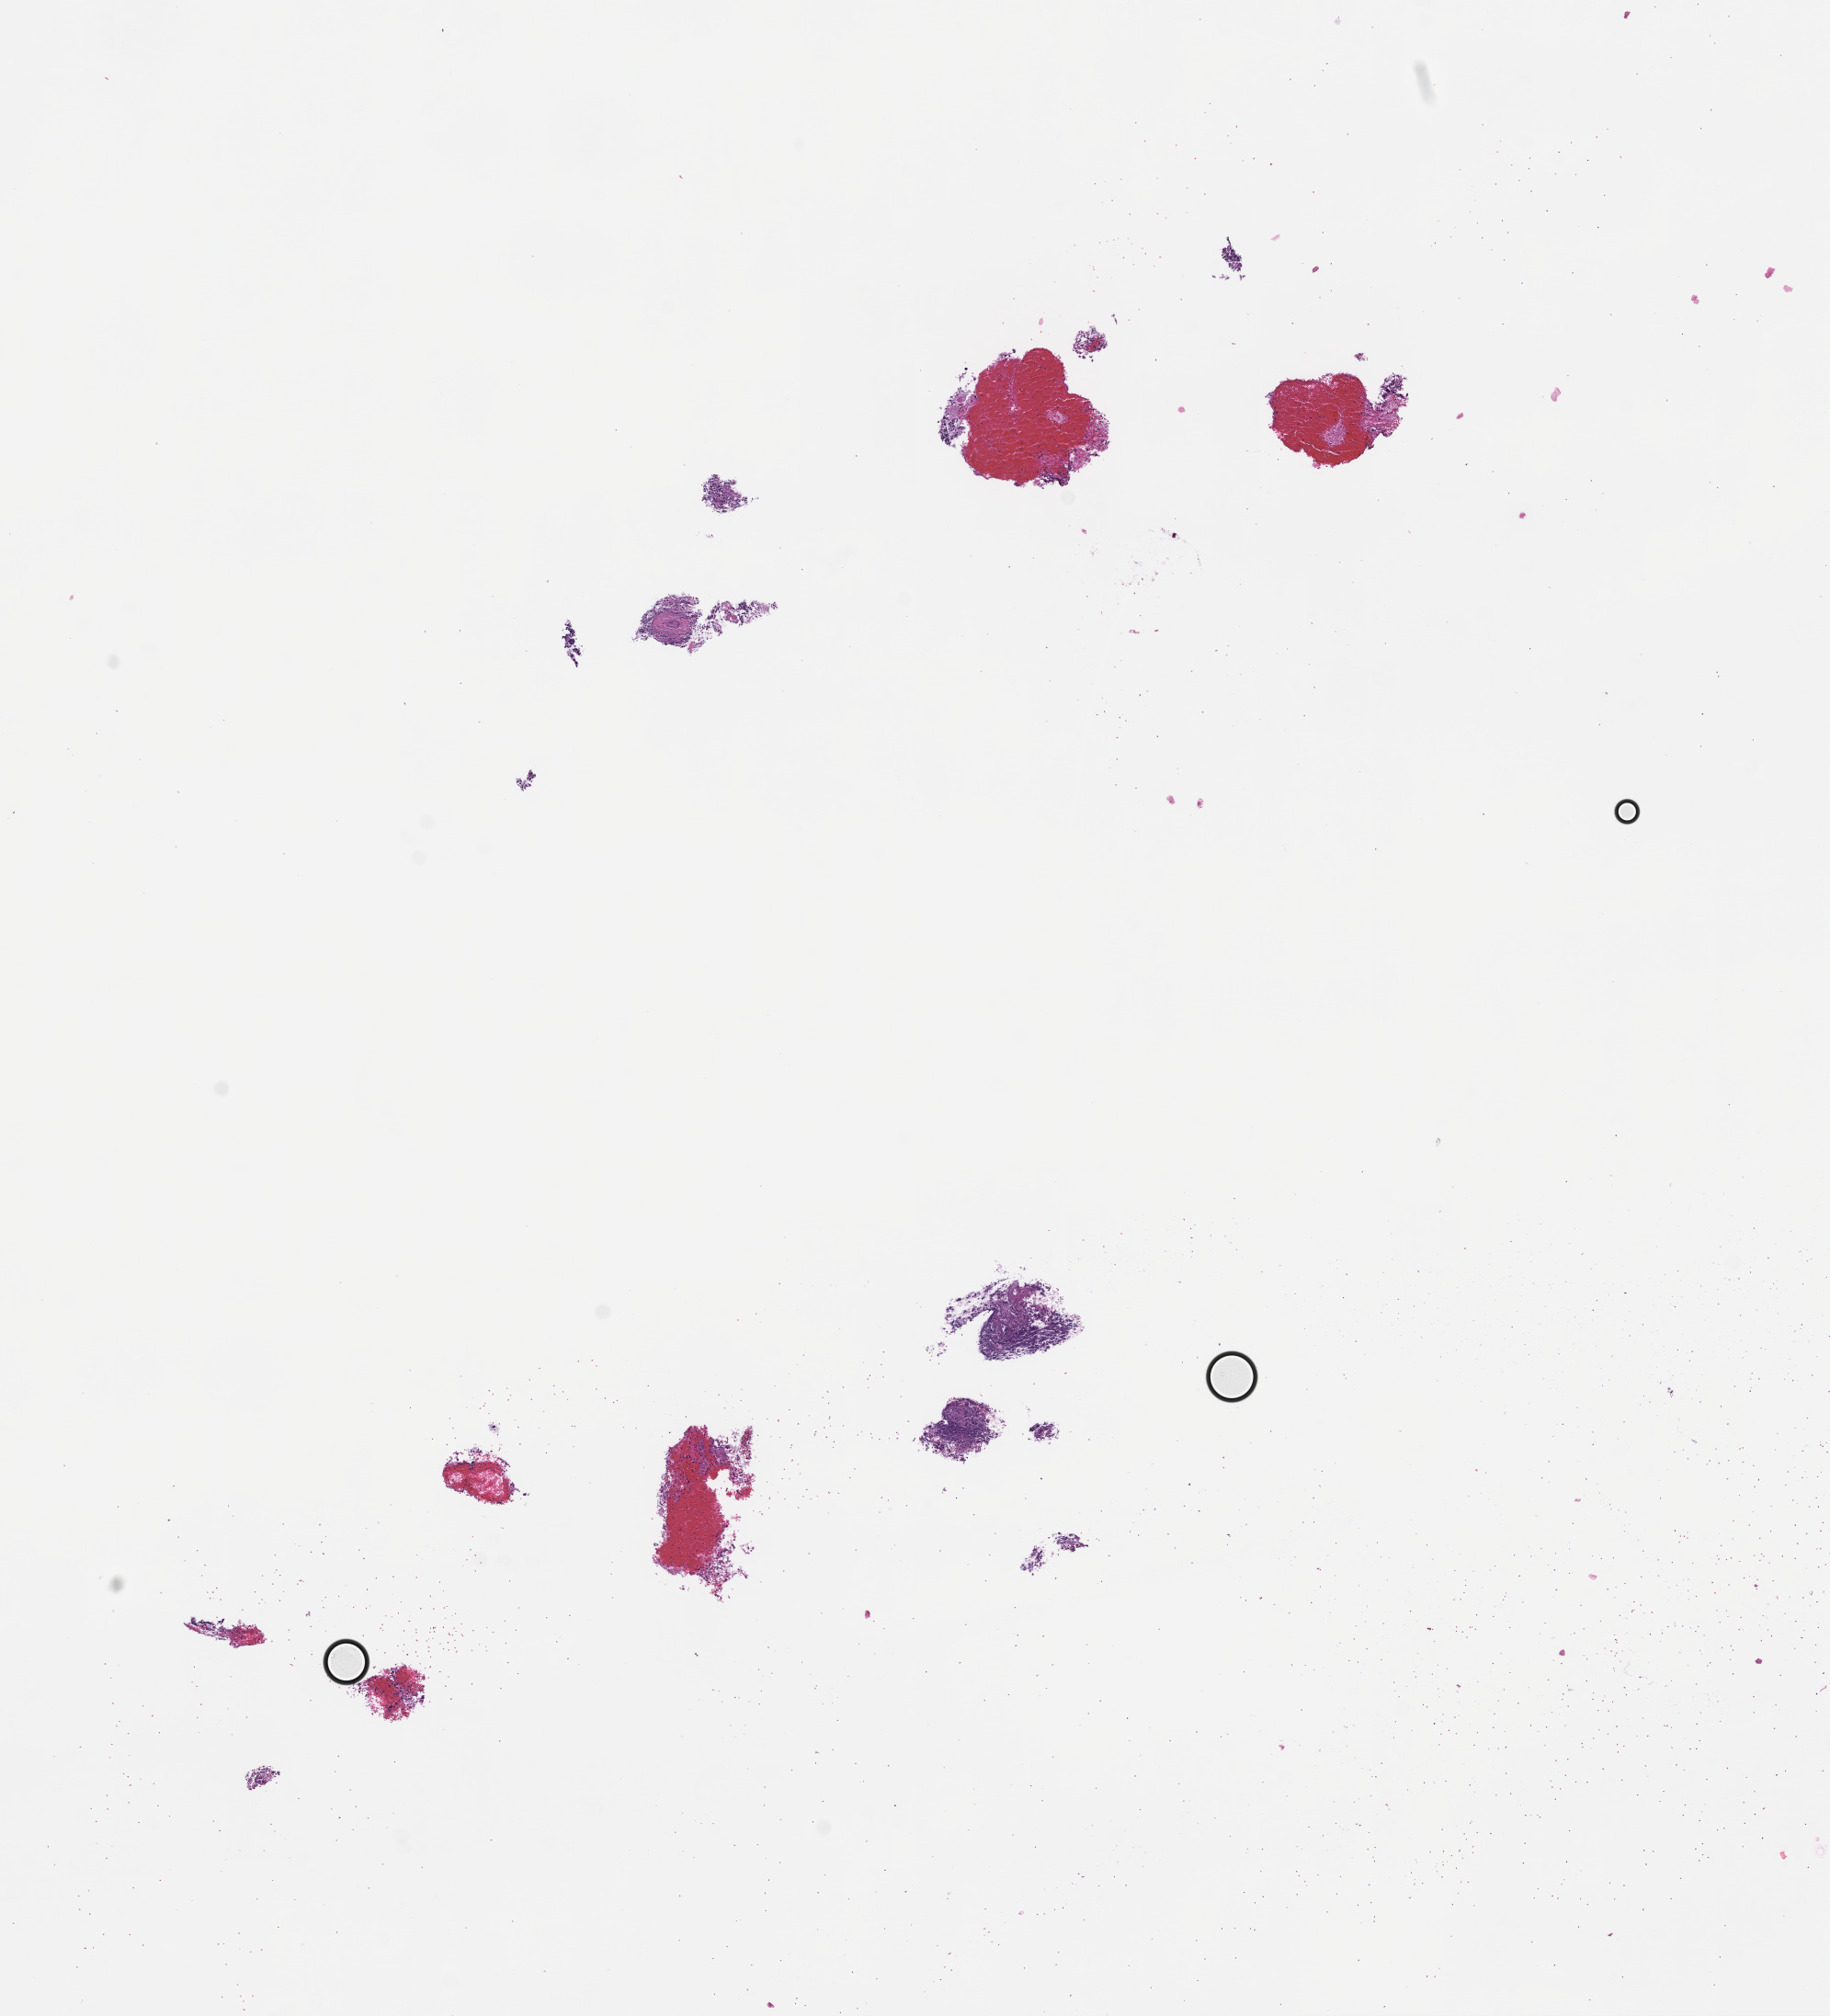
H&E whole-slide image — shown as a low-resolution overview of the whole scanned area (about 8.0 x 8.9 mm); formalin-fixed, paraffin-embedded (FFPE) tissue; tissue site: lung. Patient sex: male.
This section: primary tumor. Diagnosis: Non-Small Cell Lung Carcinoma.